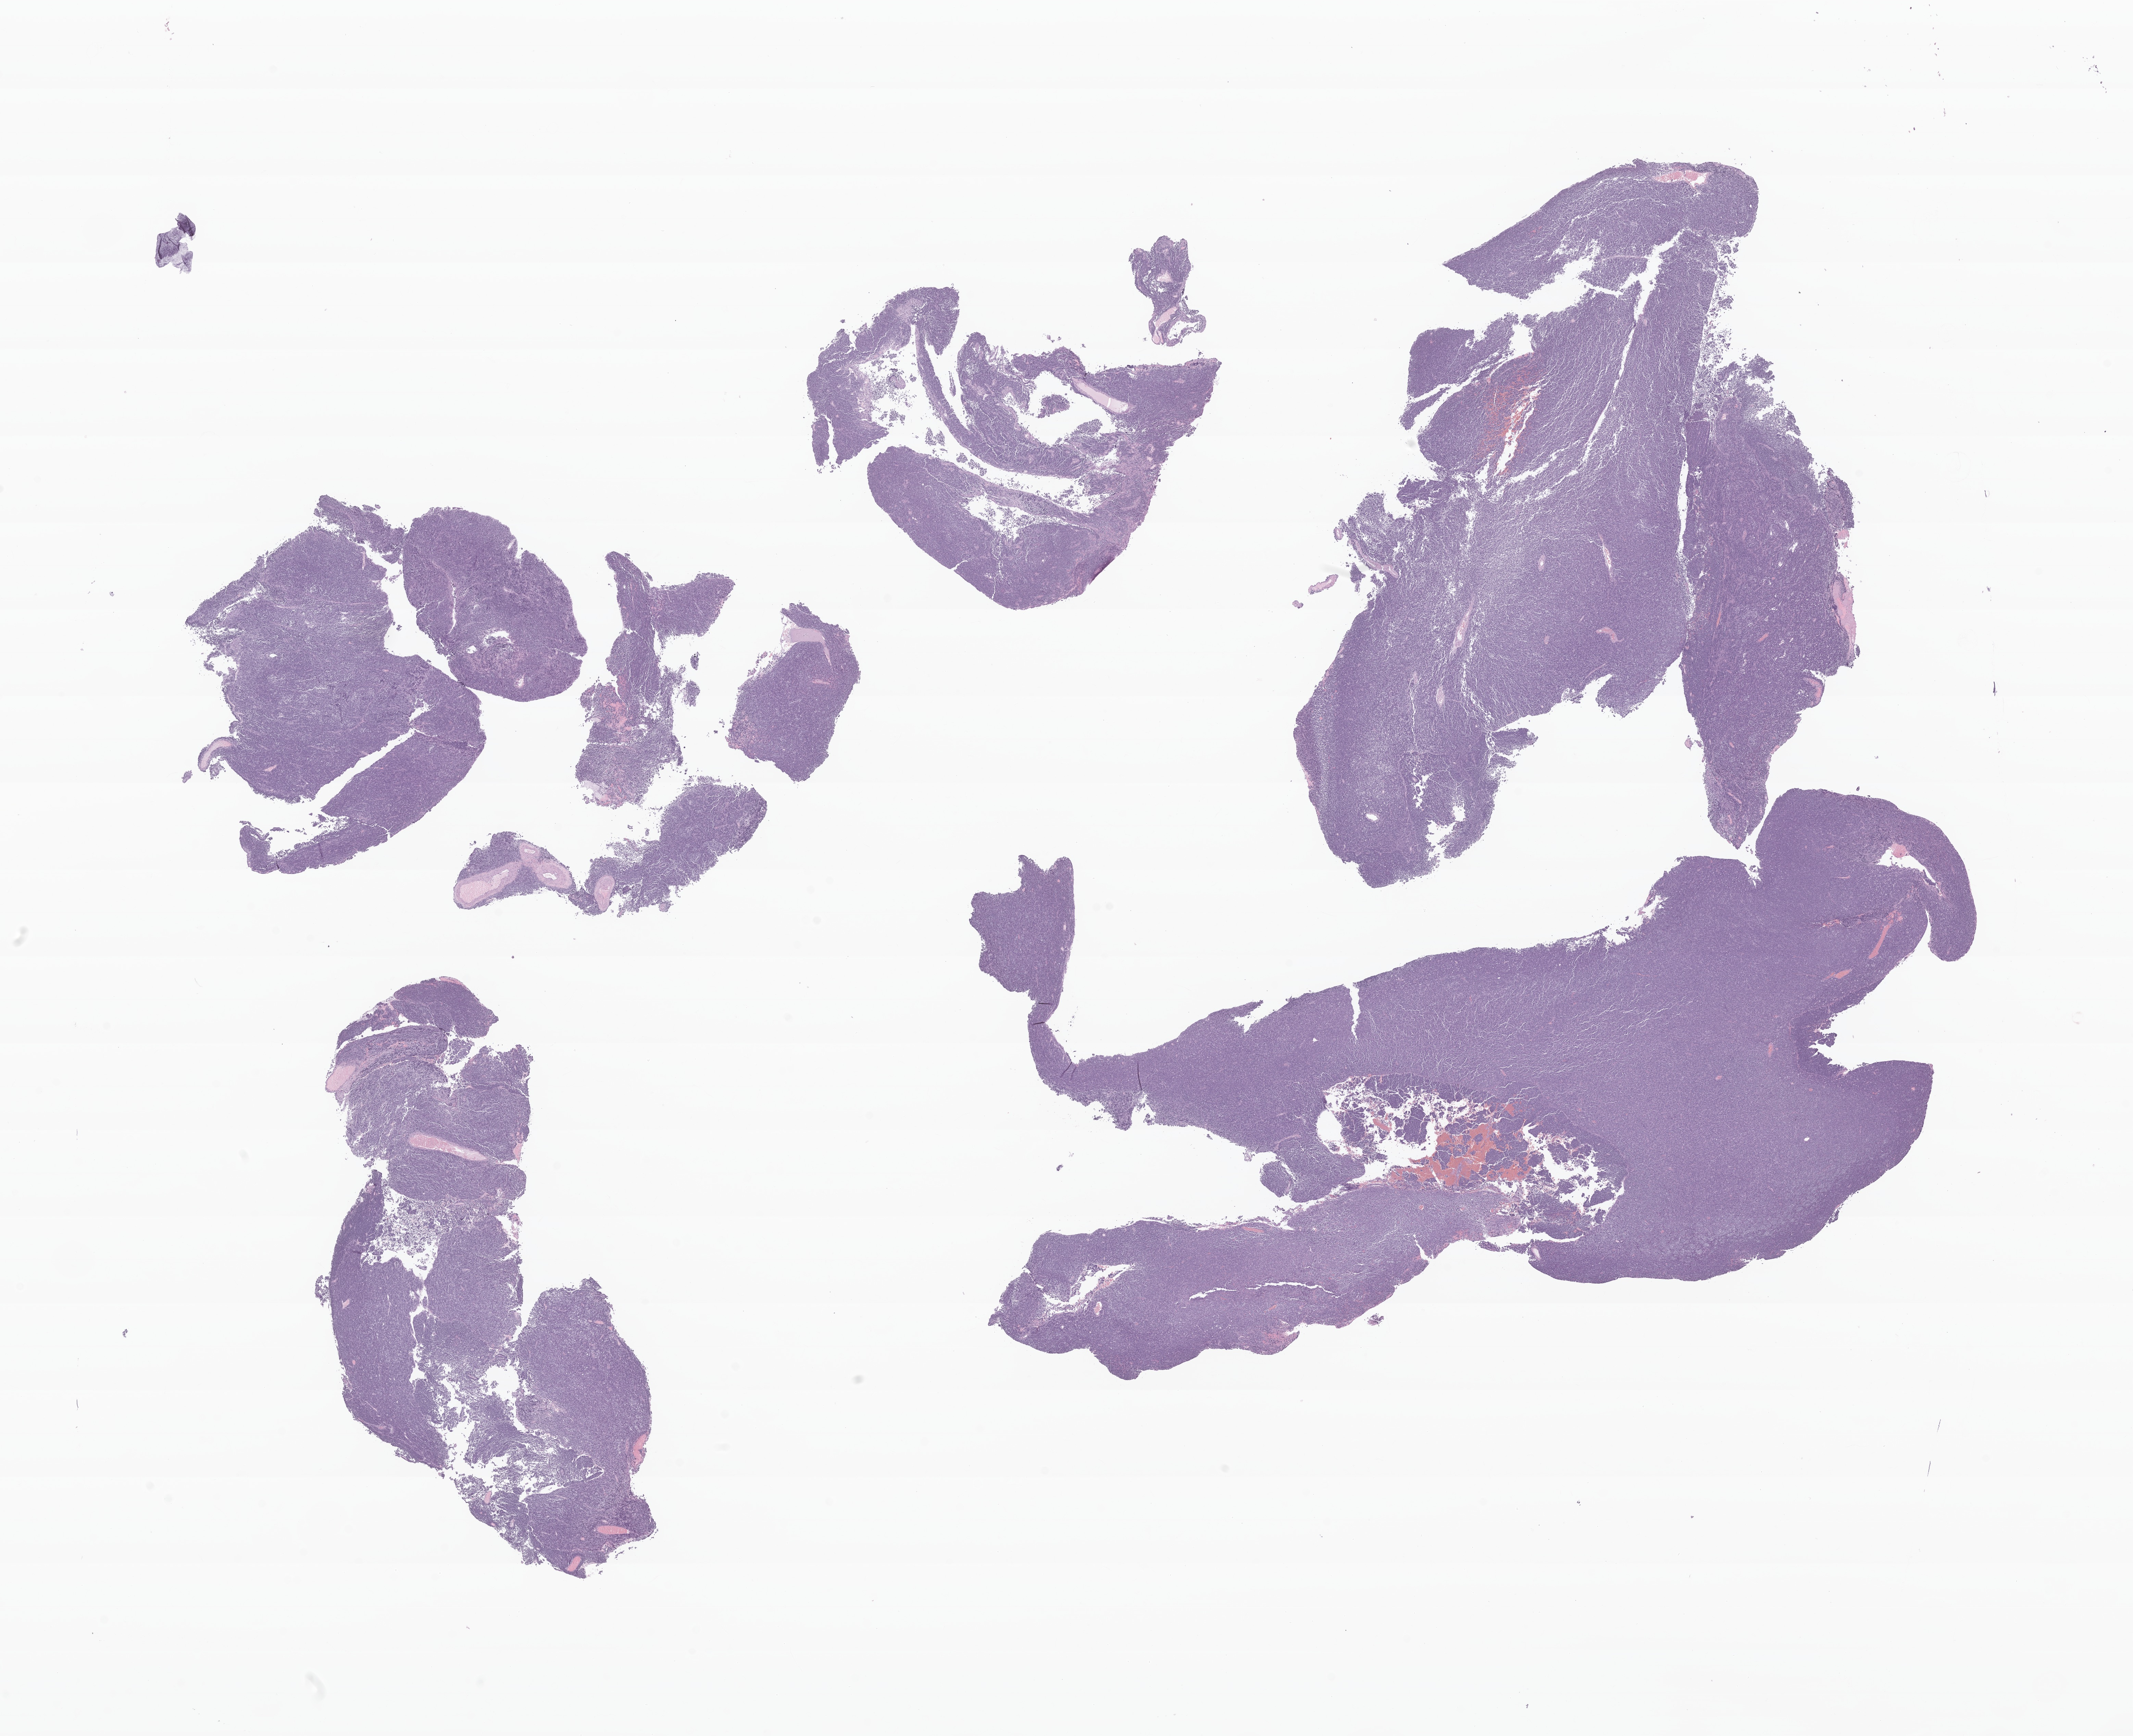
H&E whole-slide image of tumor tissue from the brain, low-resolution overview of the scanned area, about 26.2 x 21.3 mm; formalin-fixed, paraffin-embedded (FFPE) tissue. Patient: female, age 210 months (17 years 6 months).
Recorded diagnosis: Desmoplastic nodular medulloblastoma.